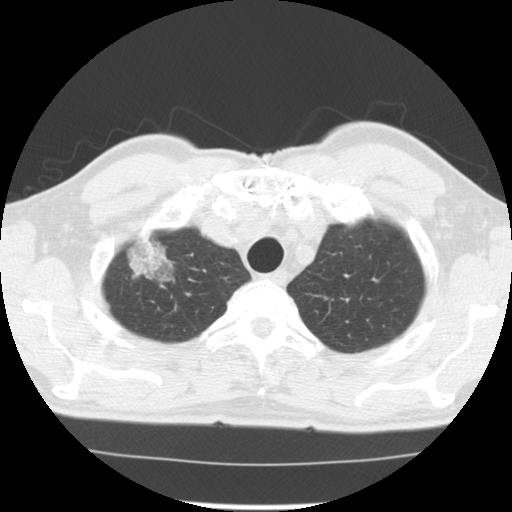
Low-dose screening chest CT, axial slice; third screening round (two years after baseline); lung window (W 1500 / L -600 HU); 2.5 mm slice thickness; 120 kVp. Male participant, aged 64 years at enrolment. Former smoker at enrolment.
Expert reader's lesion annotation, bounding box [x1, y1, x2, y2] px = [121, 233, 192, 292]. The screening reader recorded 3 non-calcified nodules or masses ≥4 mm on this exam (right upper lobe, right lower lobe, left upper lobe); which of them this box marks is not recorded. Official screen result: positive, other. Lung cancer was diagnosed 30 days after this screen: adenocarcinoma, NOS, right upper lobe, well differentiated (G1), stage IB (AJCC 6th edition), 45 mm at pathology.